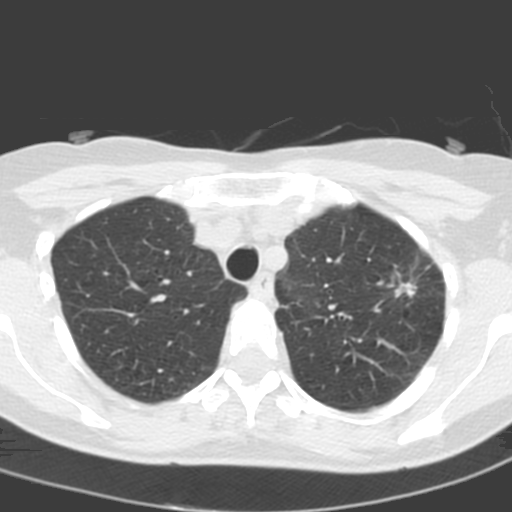
Chest CT (low-dose screening protocol), one axial image; first (baseline) screen; lung window (W 1500 / L -600 HU); 3.2 mm slice thickness; slice 41 of 193 in the series; 512 × 512 image matrix, field of view 272 × 272 mm. Female participant, aged 58 years at enrolment. Current smoker at enrolment.
- Expert reader's lesion annotation, bounding box [x1, y1, x2, y2] px = [379, 262, 432, 314].
- The exam's reader record, not a measurement of the box and not confirmed to be the same lesion: non-calcified nodule or mass ≥4 mm, left upper lobe, 14 × 10 mm, spiculated (stellate) margins, soft tissue attenuation.
- Official screen result: positive, change unspecified: nodule(s) >= 4 mm or enlarging nodule(s), mass(es), or other non-specific abnormalities suspicious for lung cancer.